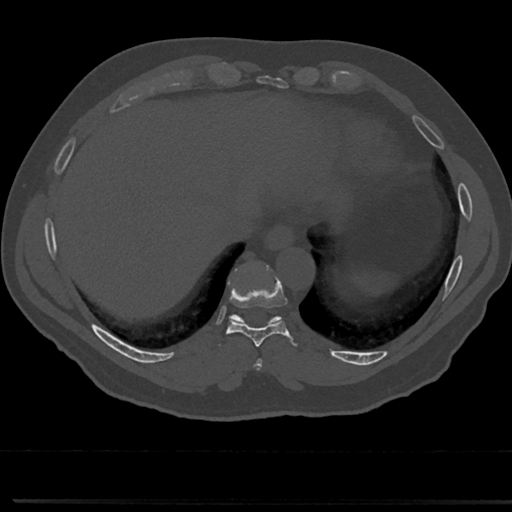
CT including the spine, one axial slice. Position 295 of 817 along the scan axis. Reconstruction kernel Br40s/3. Bone window (W 1800 / L 400 HU). 0.5 mm slice thickness. 512 × 512 image matrix. Patient: male, 61 years. Case-level facts recorded for this patient, not image findings: primary cancer: prostate.
Structures marked on this image (semi-automatic segmentation, software-assisted and operator-edited):
- T8 vertebra: box from (x=251, y=329) to (x=278, y=360) px
- T9 vertebra: (x=217, y=266)–(x=295, y=349)